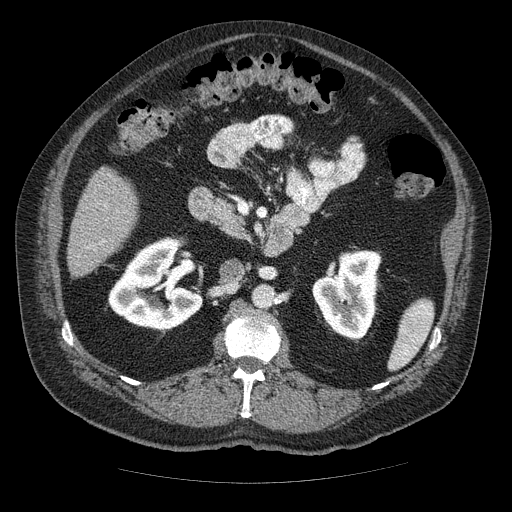
Contrast-enhanced abdominal CT (liver protocol), one axial slice; slice 15 of 85 in the series (ordered by position); reconstruction kernel STANDARD; 120 kVp; soft-tissue window (W 400 / L 40 HU); 2.5 mm slice thickness; 512 × 512 image matrix, field of view 420 × 420 mm. Case-level facts recorded for this patient, not image findings: diagnosis: hepatocellular carcinoma (patient treated with transarterial chemoembolisation; whether this scan precedes or follows treatment is not stated here); TNM stage (as recorded): Stage-IIIA; Child-Pugh class: A.
Outlined on this slice (semi-automatically segmented with operator editing):
- liver parenchyma outside the tumour (the mass and vessels are separate outlines, so this box may not span the whole liver): box from (x=68, y=166) to (x=136, y=276) px